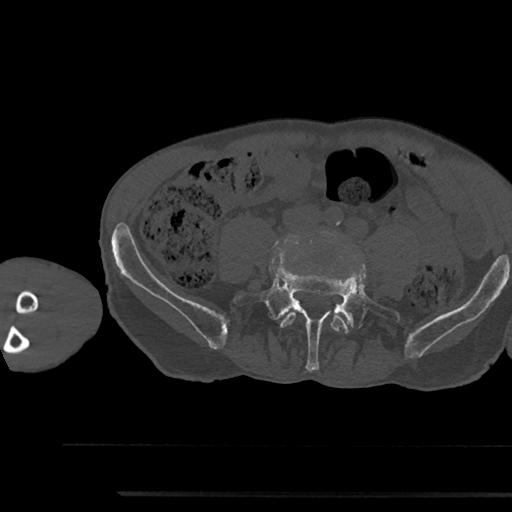
CT including the spine, one axial slice; slice 367 of 797 in the series (ordered by position); 120 kVp; bone window (W 1800 / L 400 HU); 0.5 mm slice thickness; 512 × 512 image matrix, field of view 367 × 367 mm. Patient: male, 79 years. Case-level facts recorded for this patient, not image findings: primary cancer: prostate.
Annotated regions visible in this slice (semi-automatically segmented with operator editing):
- L4 vertebra: bounding box <280,311,349,333> (left, top, right, bottom; pixels)
- L5 vertebra: <233,263,400,371>